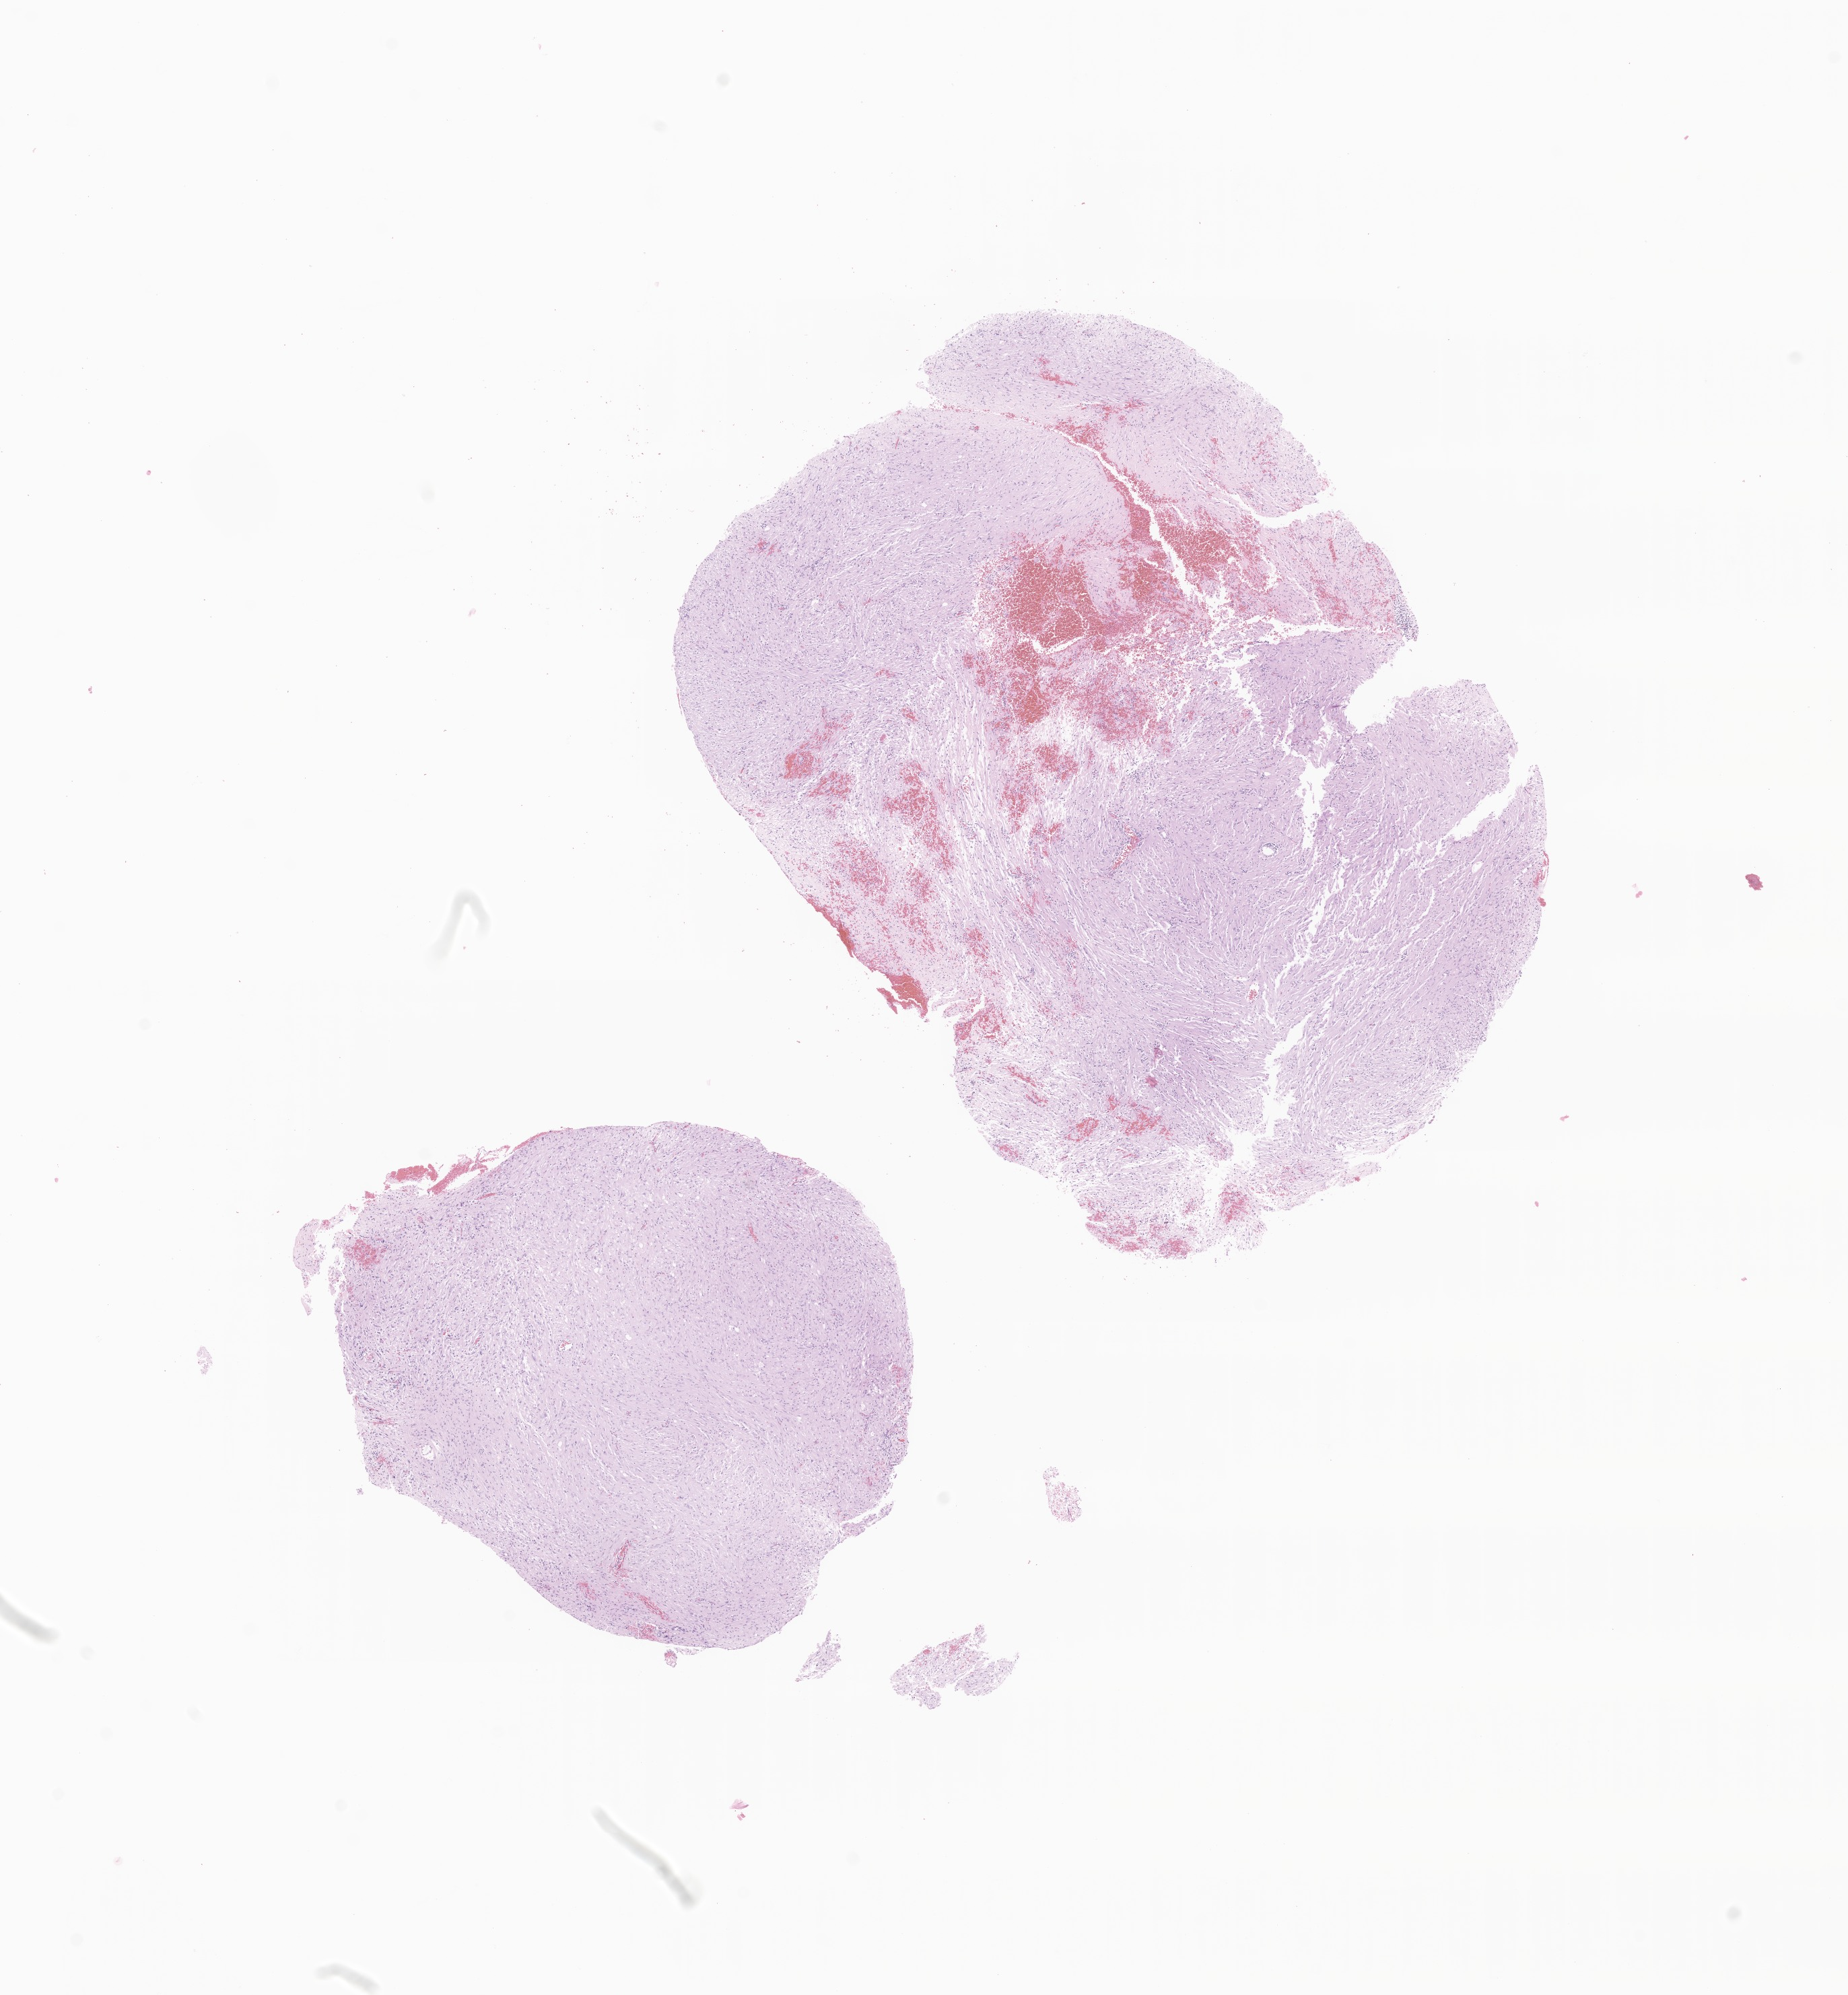
H&E whole-slide image of tumor tissue from the temporal lobe — a low-resolution overview of the entire scanned area, about 11.6 x 12.5 mm. FFPE section. Male patient, age 192 months (16 years).
• diagnosis: Ganglioglioma, NOS